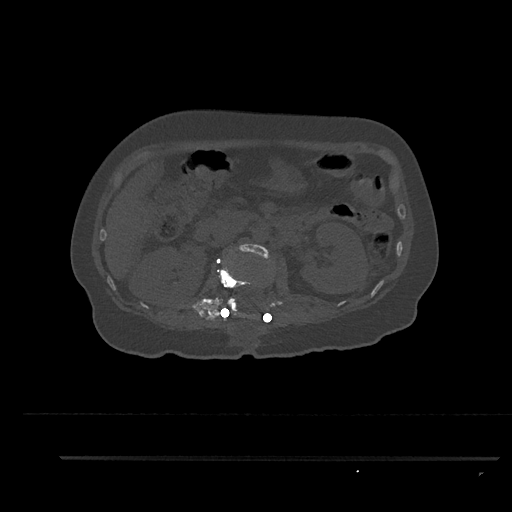
CT including the spine, one axial slice; reconstruction kernel Br40s/3; bone window (W 1800 / L 400 HU); 0.5 mm slice thickness; 512 × 512 image matrix, field of view 408 × 408 mm. Female patient, age 44 years. Case-level facts recorded for this patient, not image findings: primary cancer: renal.
Structures marked on this image (semi-automatic segmentation, software-assisted and operator-edited):
- L1 vertebra: box from (x=218, y=260) to (x=251, y=317) px
- L2 vertebra: (x=226, y=244)–(x=271, y=314)